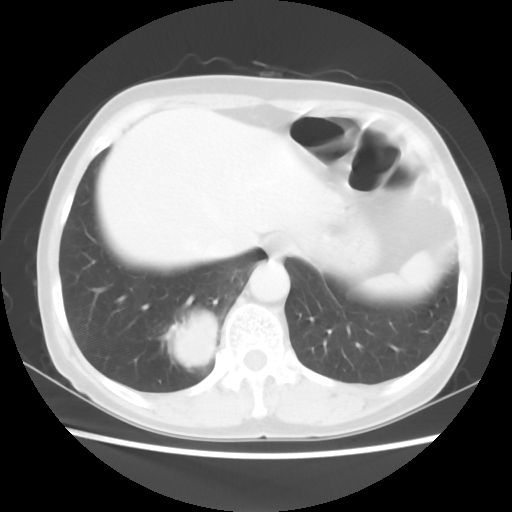
Chest CT, one axial slice. Slice 10 of 56 in the series (ordered by position). Reconstruction kernel STANDARD. 120 kVp. Lung window (W 1500 / L -600 HU). 512 × 512 image matrix, field of view 332 × 332 mm. Female patient, age 66 years. From the clinical record (not read from this slice): clinical TNM (as recorded): T2 N3 M0; histopathological grade: G3.
Annotated regions visible in this slice (bounding box drawn by a radiologist):
- lung tumour (recorded histology: small cell carcinoma): bounding box <166,300,220,383> (left, top, right, bottom; pixels)